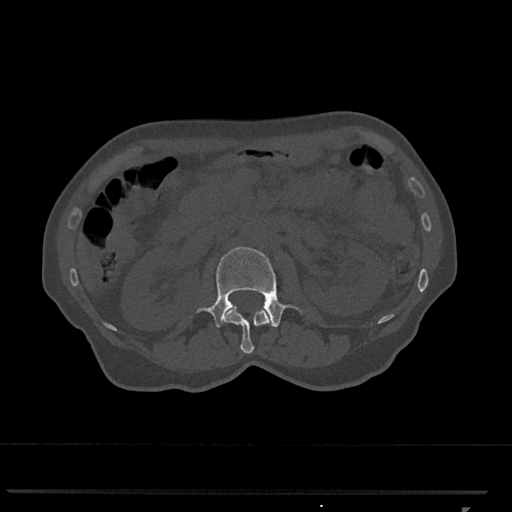
CT including the spine, one axial slice. Slice 363 of 793 in the series (ordered by position). Reconstruction kernel Br40s/3. Bone window (W 1800 / L 400 HU). 0.5 mm slice thickness. 512 × 512 image matrix, field of view 380 × 380 mm. Female patient, age 62 years. Case-level facts recorded for this patient, not image findings: primary cancer: renal.
Outlined on this slice (semi-automatic segmentation, software-assisted and operator-edited):
- L1 vertebra: bounding box [x1, y1, x2, y2] px = [224, 308, 272, 354]
- L2 vertebra: [197, 247, 302, 327]